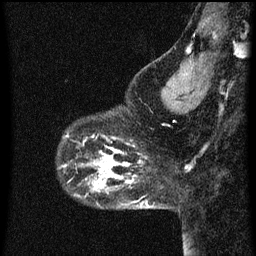
Breast MRI (dynamic contrast-enhanced), one sagittal slice; slice 14 of 60 in the series (ordered by position); dynamic contrast-enhanced series, image 2 of 3 at this slice position (ordered by acquisition); 1.5 T; TE 4.2 ms, TR 8 ms; 2 mm slice thickness; 256 × 256 image matrix, field of view 180 × 180 mm. Female patient, age 43 years.
Annotated regions visible in this slice (semi-automatic segmentation, software-assisted and operator-edited):
- analysis volume of interest (the breast-tissue region the enhancement analysis was run in; not a lesion): bounding box [x1, y1, x2, y2] px = [59, 116, 101, 155]
- tumour enhancement mask (voxels above the 70 % enhancement threshold inside the analysis volume of interest): [67, 136, 101, 153]